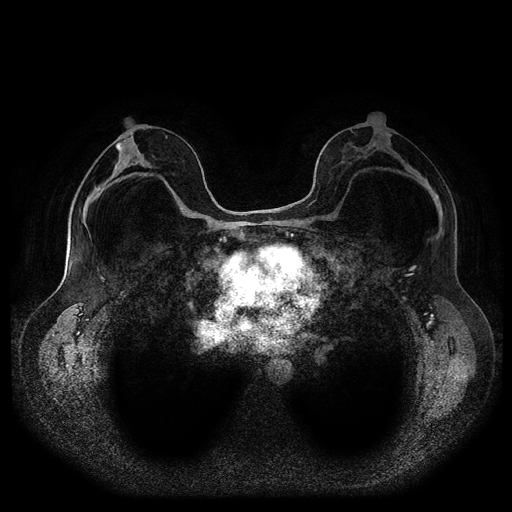
Breast MRI (dynamic contrast-enhanced, multi-phase), one axial slice. Position 55 of 116 along the scan axis. Dynamic contrast-enhanced series, time point 2 of 5 at this slice position (early post-contrast). 1.5 T. TE 2.6 ms, TR 5.3 ms. 512 × 512 image matrix, field of view 360 × 360 mm. Female patient, age 46 years.
Structures marked on this image (semi-automatically segmented with operator editing):
- breast lesion (labelled 'tumour' in the annotation; benign lesions carry a separate 'benign' label): bounding box (x1, y1, x2, y2) in pixels: (116, 140, 125, 151)